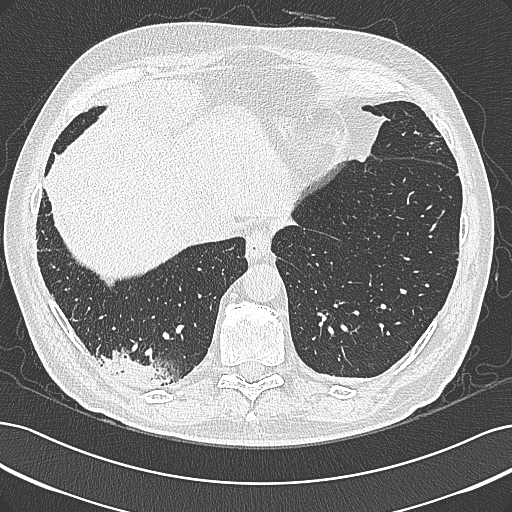
Chest CT (low-dose screening protocol), one axial image; baseline annual screen; lung window (W 1500 / L -600 HU); 1 mm slice thickness; lung (sharp) reconstruction kernel (B80f); slice 233 of 355 in the series; 512 × 512 image matrix. Male, age 68 years at enrolment. Former smoker at enrolment.
Expert reader's lesion annotation, box from (x=97, y=340) to (x=185, y=401) px. Screening reader's record for this exam: no non-calcified nodule ≥4 mm recorded. Official screen result: negative screen, significant abnormalities not suspicious for lung cancer.